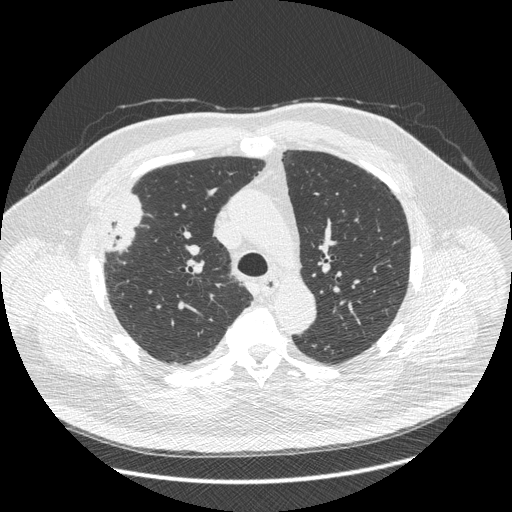
Low-dose screening chest CT, one axial slice; position 298 of 426 along the scan axis; reconstruction kernel STANDARD; 120 kVp; lung window (W 1500 / L -600 HU); 1.25 mm slice thickness; 512 × 512 image matrix, field of view 400 × 400 mm.
Structures marked on this image (outlined manually by an expert reader):
- lesion 1 (tumor, upper lobe of right lung): bounding box [x1, y1, x2, y2] px = [104, 194, 142, 252]